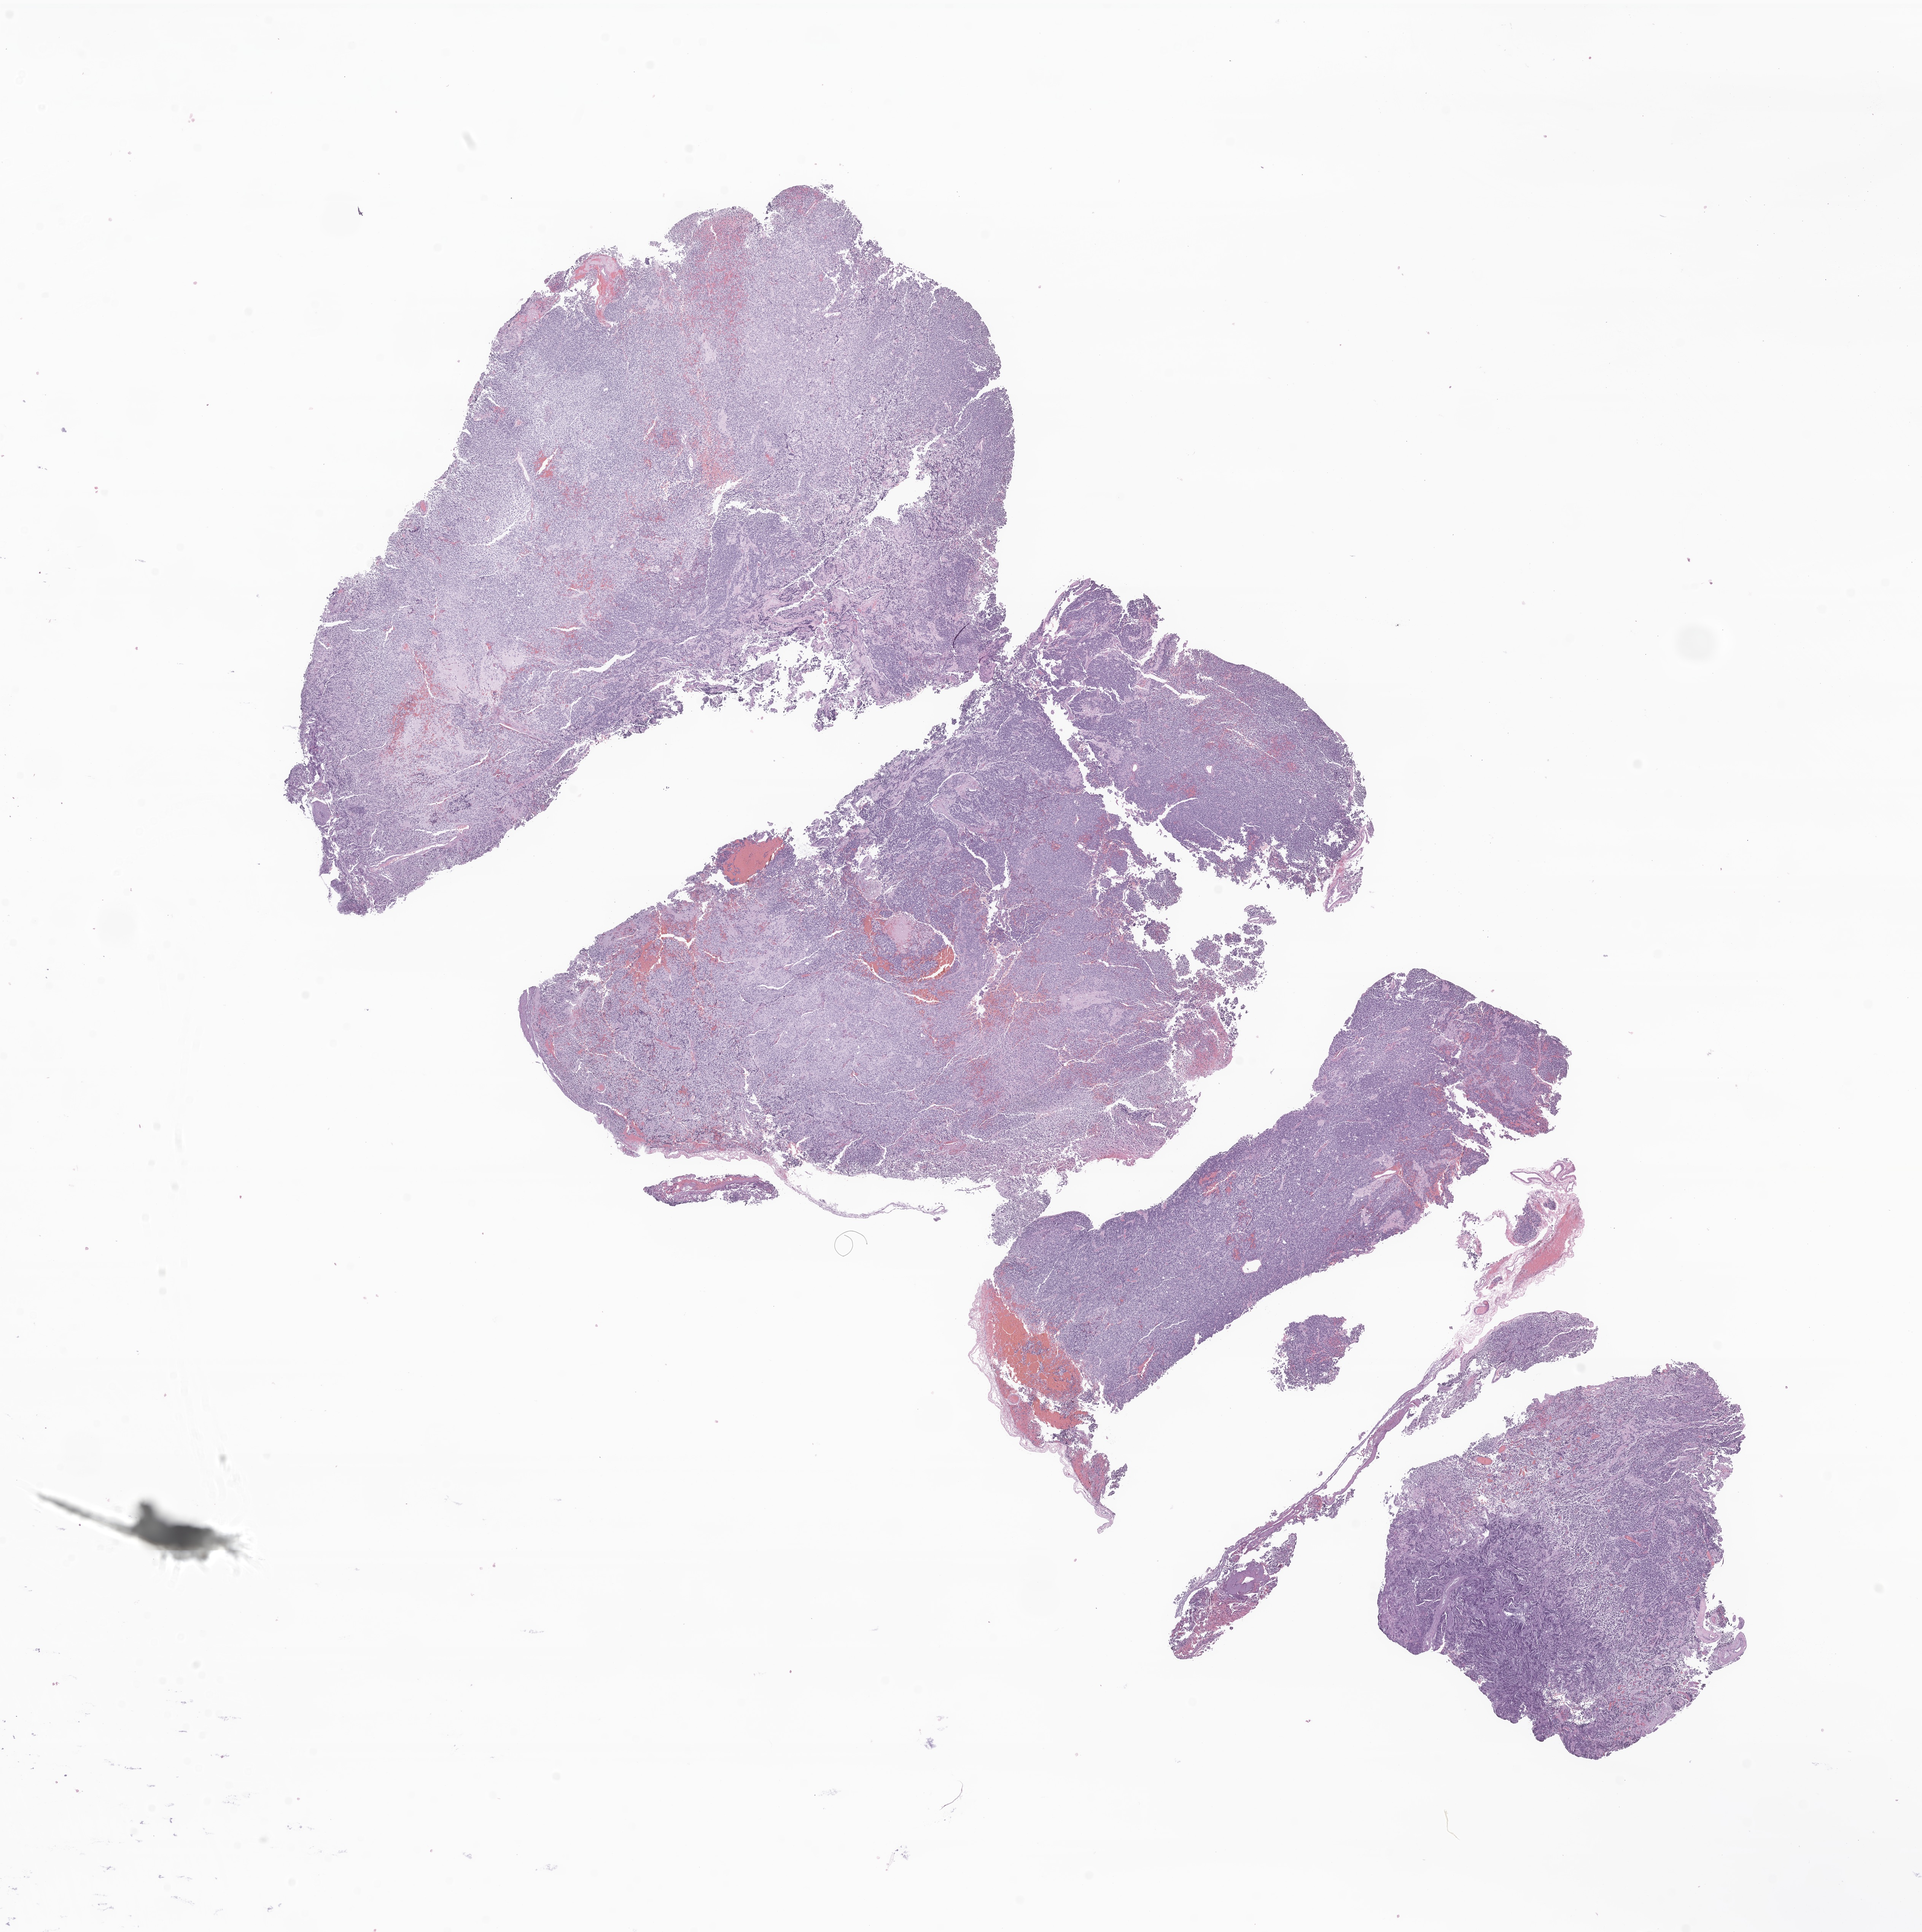
Whole-slide image, hematoxylin and eosin (H&E) stain of tumor tissue from the central nervous system, a low-resolution overview of the entire scanned area, about 21.3 x 21.4 mm; formalin-fixed, paraffin-embedded (FFPE) tissue. Patient female; age 159 months (13 years 3 months).
* diagnosis (ICD-O-3 morphology term): Neoplasm, malignant